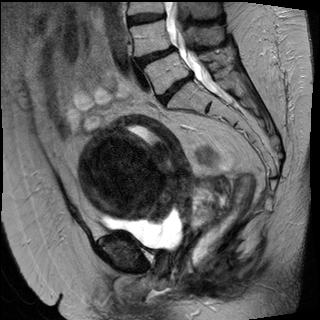
Pelvic MRI for cervical cancer, one sagittal slice. Slice 26 of 50 in the series (ordered by position). T2-weighted. 1.5 T. TE 89 ms, TR 4880 ms. 4 mm slice thickness. 320 × 320 image matrix. Female patient, age 50 years.
Structures marked on this image (manually delineated by an expert):
- uterus and cervix: bounding box [x1, y1, x2, y2] px = [78, 115, 231, 244]